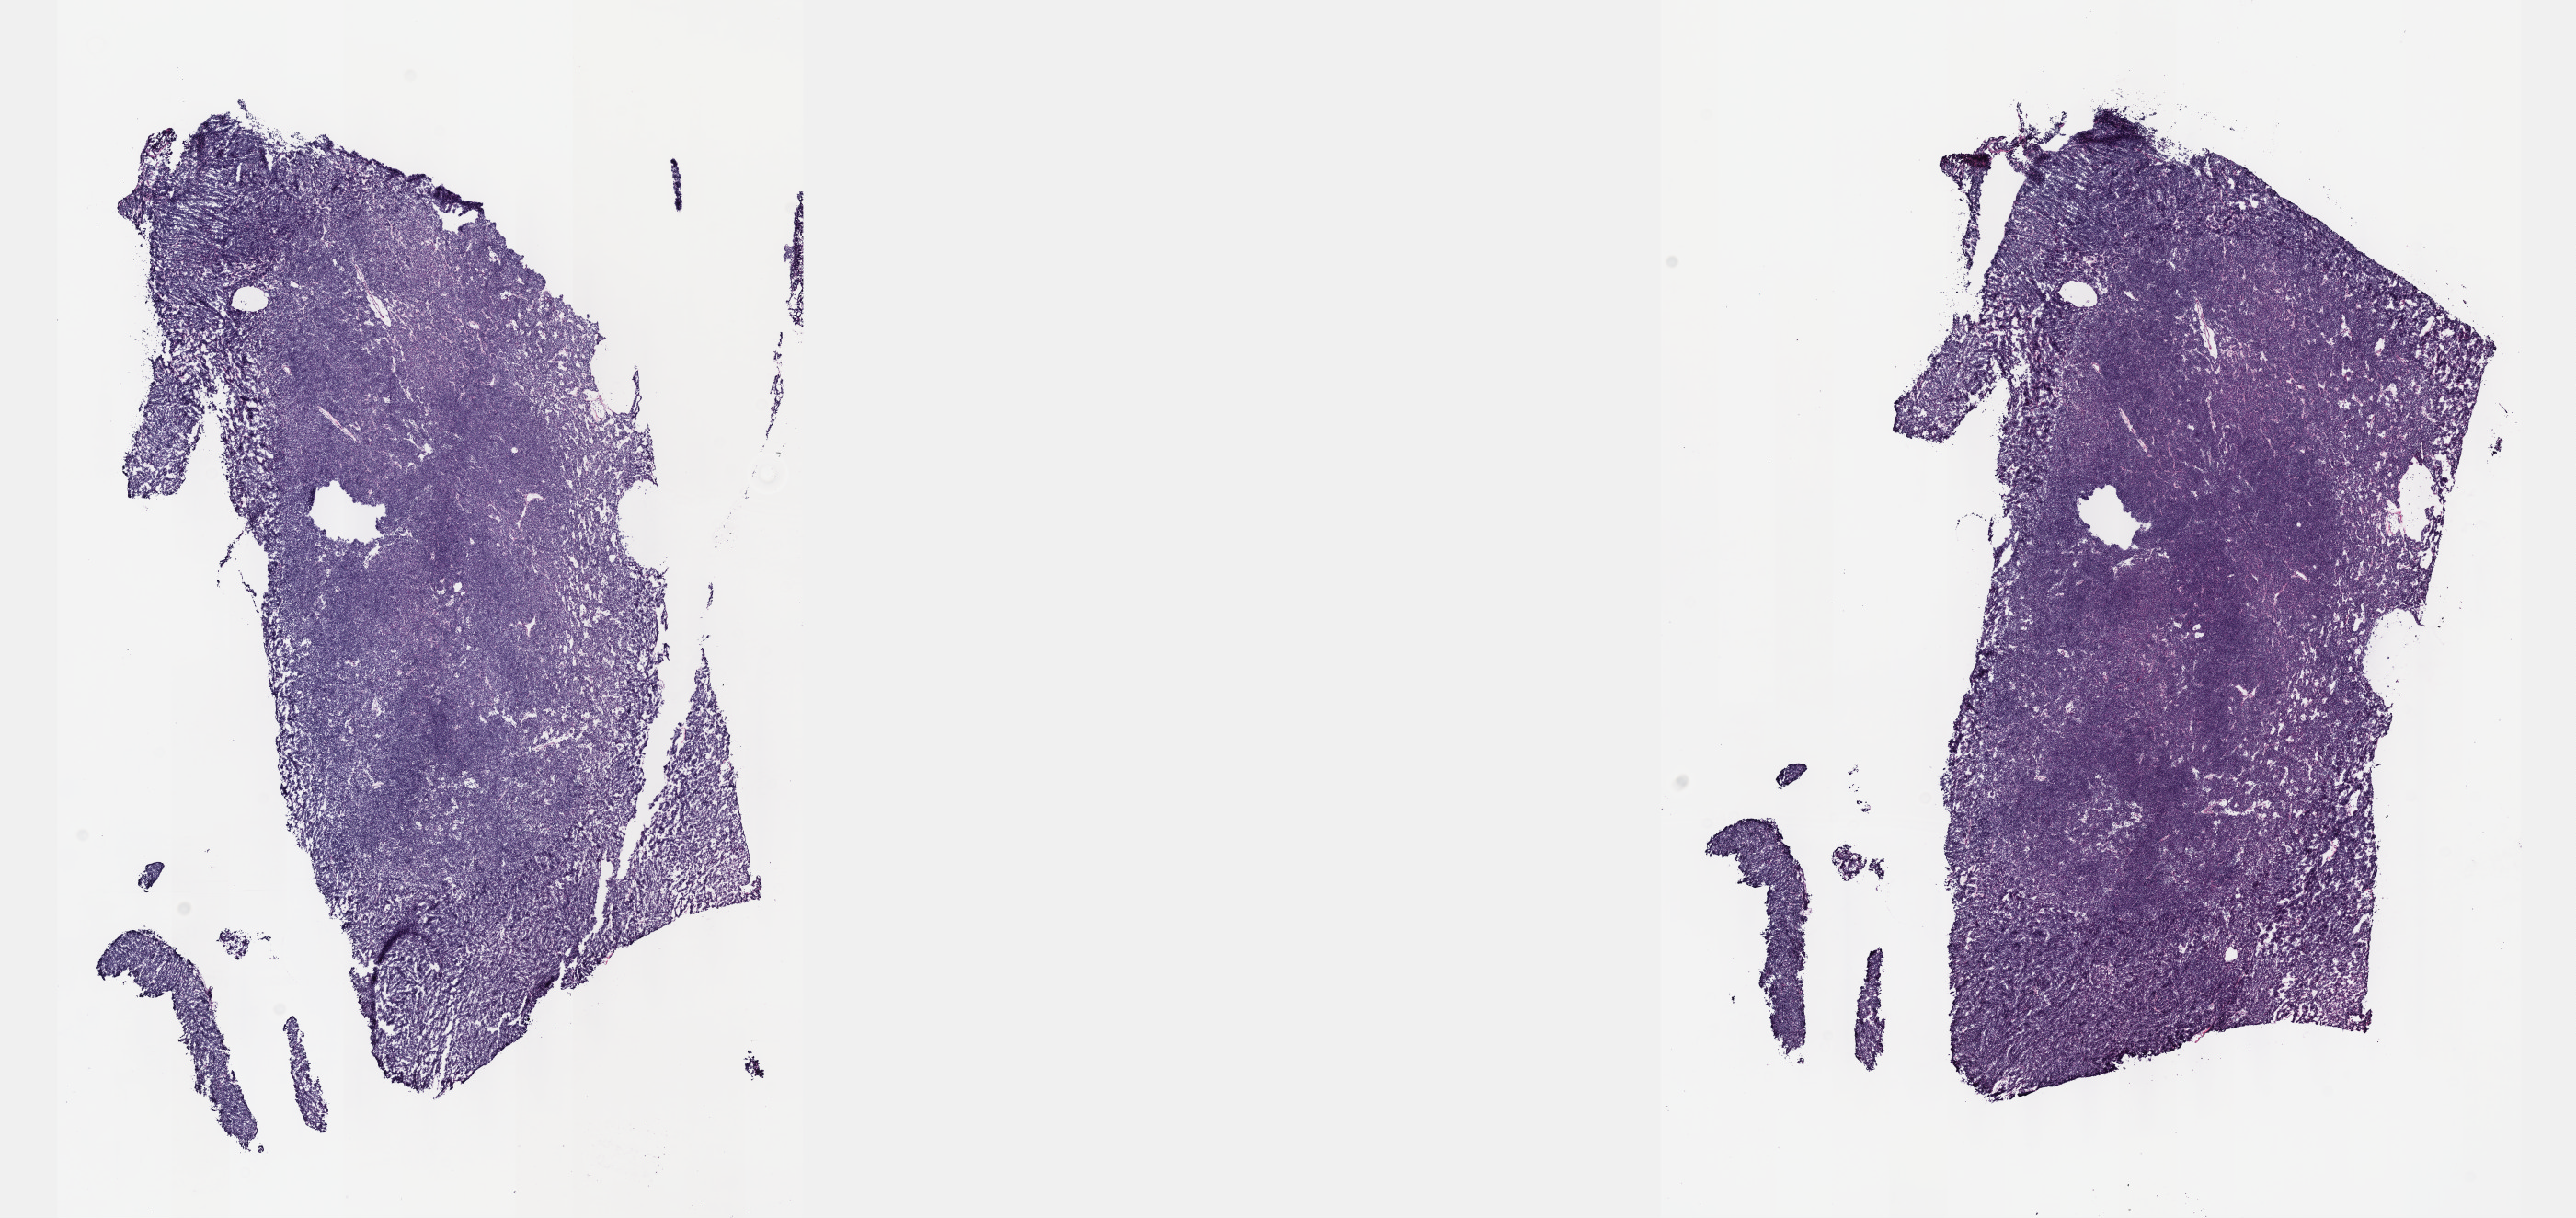
Digitized H&E-stained tissue section (whole slide), shown as a low-resolution overview of the whole scanned area (about 22.6 x 10.7 mm), frozen section, primary tumour sample from the thymus. Male patient; age at initial diagnosis 53 years. Slide review estimates, as recorded: tumour cells 85%, tumour nuclei 90%, normal cells 0%, stromal cells 15%, necrosis 0%. Inflammatory infiltration, as recorded: lymphocyte infiltration 0%, monocyte infiltration 0%, neutrophil infiltration 0%.
Histologic diagnosis: Thymoma, type B2, malignant.